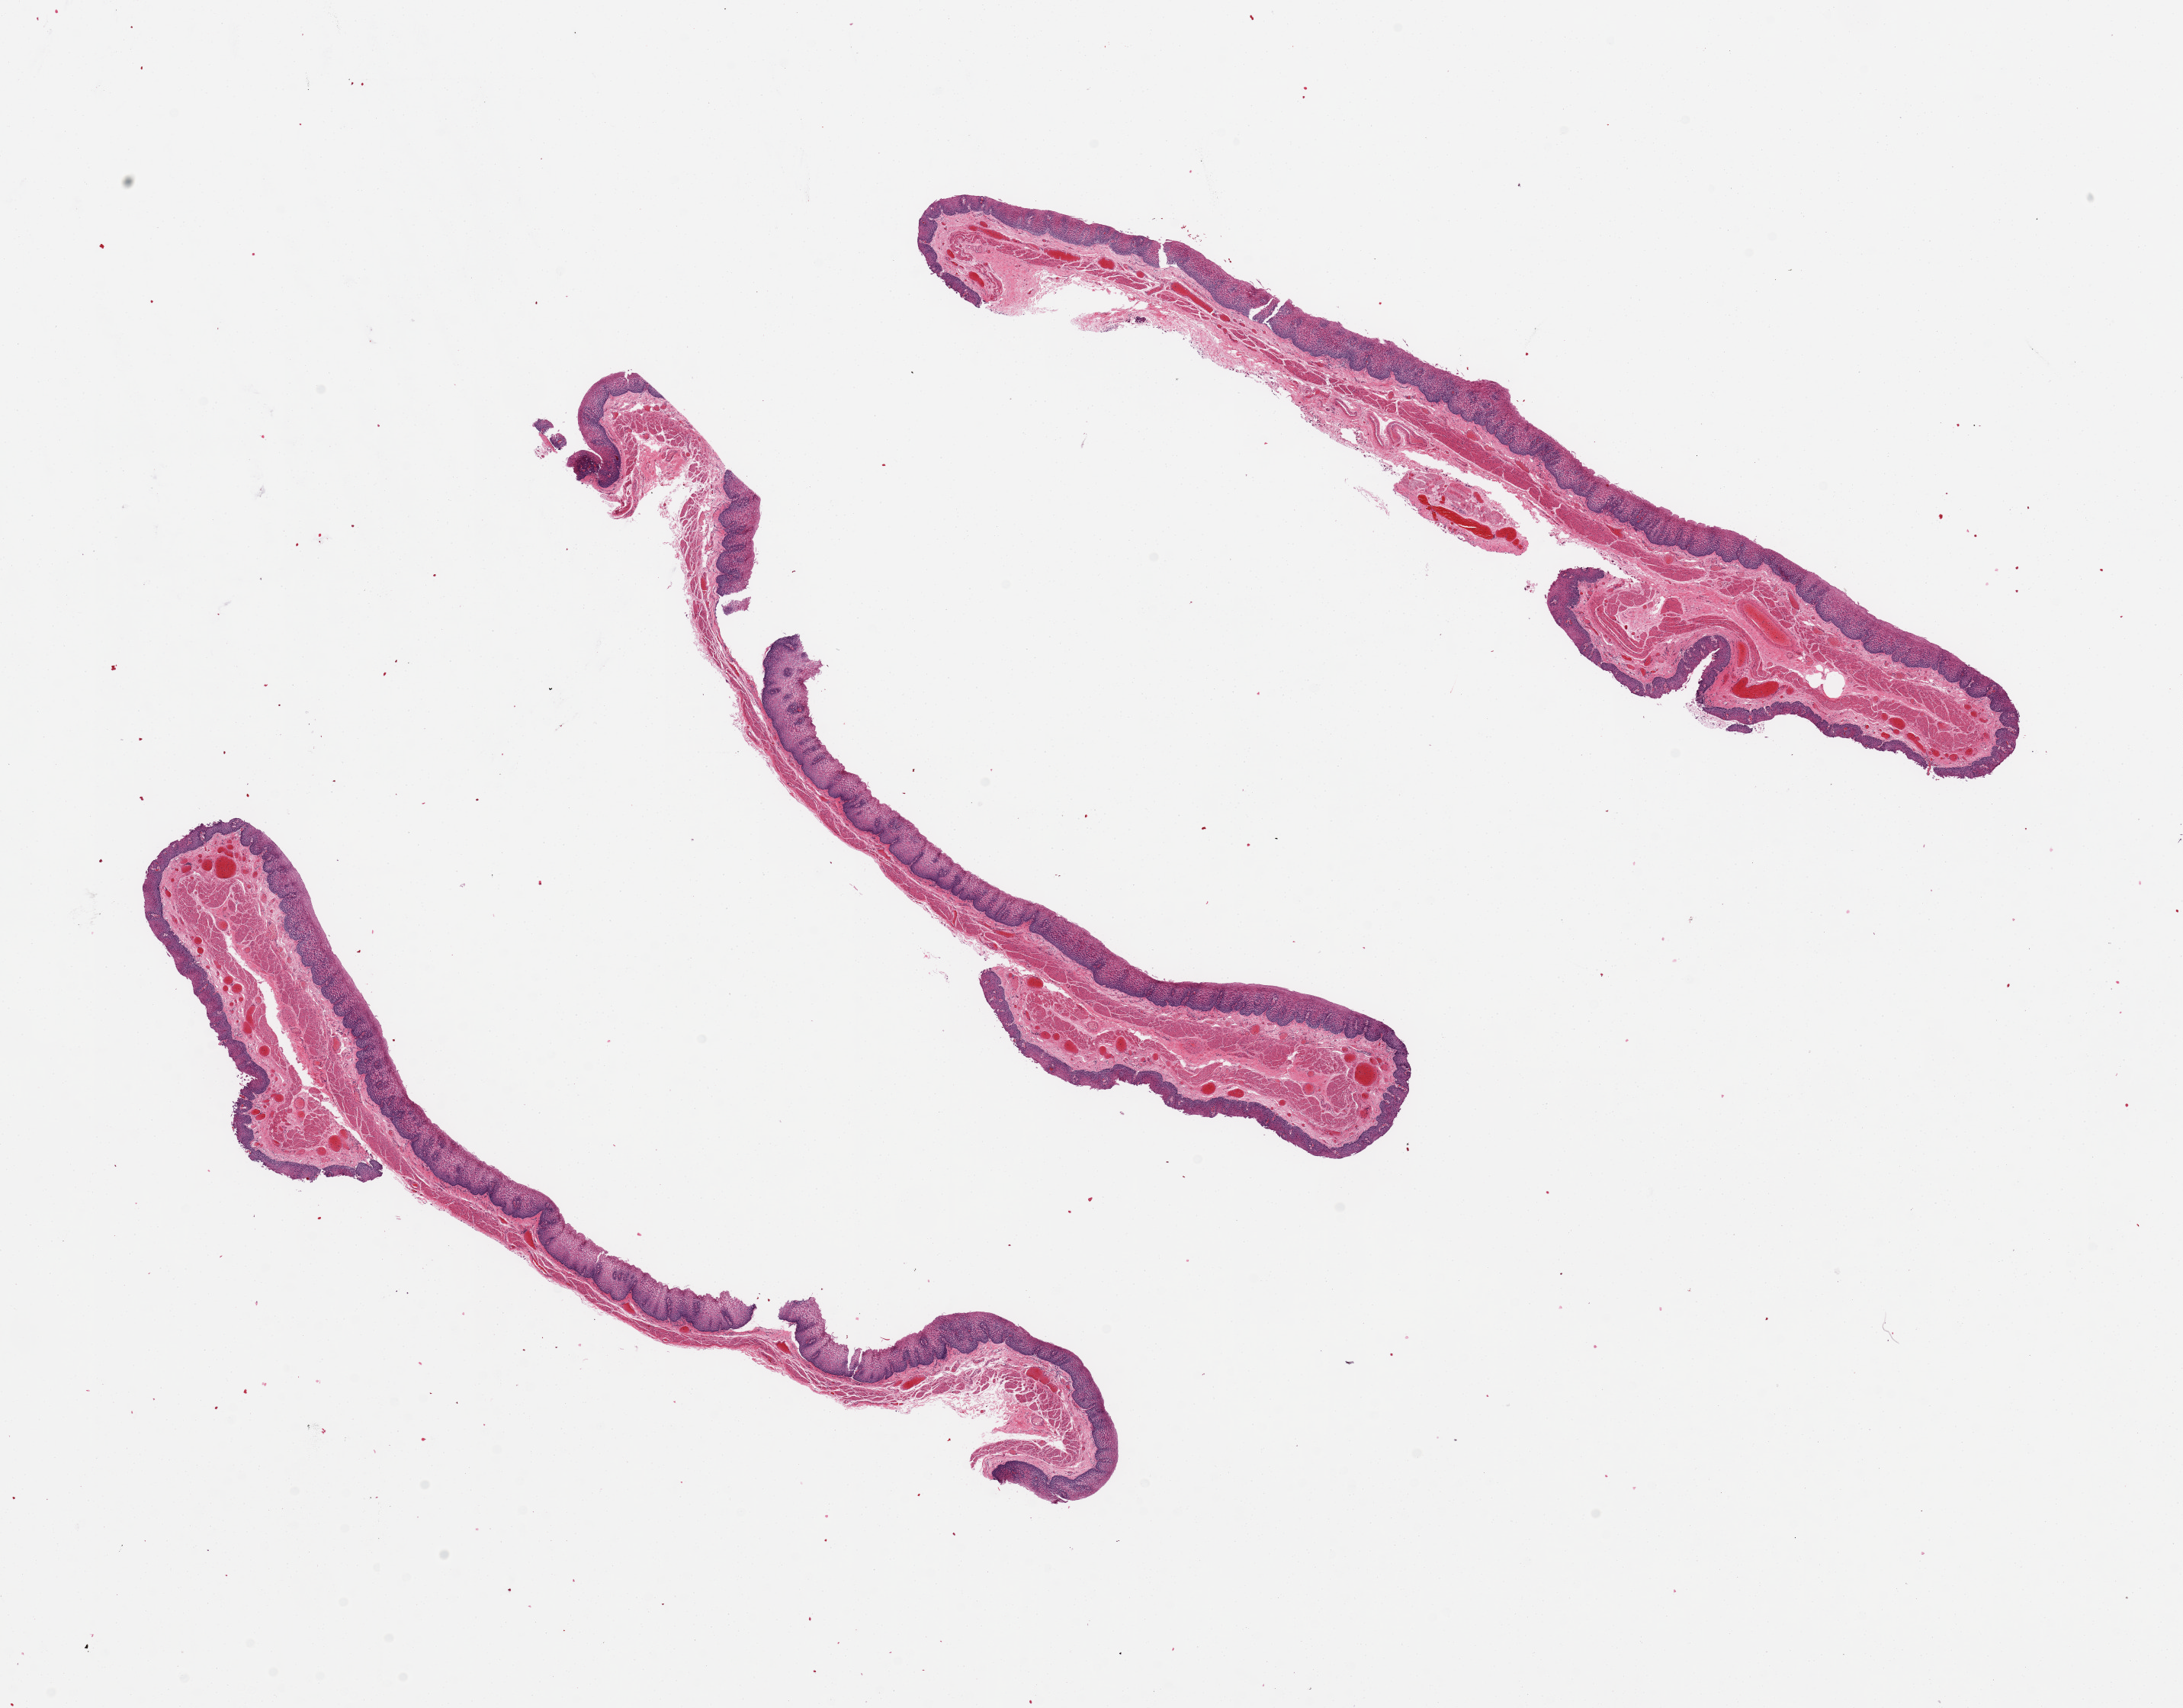
Whole-slide image, haematoxylin and eosin stain — shown as a low-resolution overview of the whole scanned area (about 22.6 x 17.7 mm, acquisition: 20x scan). PAXgene-fixed, paraffin-embedded tissue. Target tissue: esophageal mucous membrane. Donor tissue sample. Donor sex: female.
Reviewer comment on this tissue sample: 3 pieces, squamous mucosa up to ~50-70% thickness, partially sloughing.